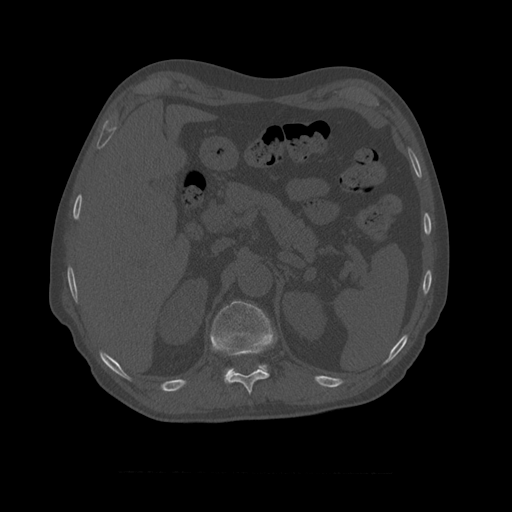
CT including the spine, one axial slice. Reconstruction kernel STANDARD. 120 kVp. Bone window (W 1800 / L 400 HU). 1.25 mm slice thickness. 512 × 512 image matrix, field of view 405 × 405 mm. Patient age 75 years. Case-level facts recorded for this patient, not image findings: primary cancer: prostate.
Structures marked on this image (semi-automatically segmented with operator editing):
- T10 vertebra: bounding box [x1, y1, x2, y2] px = [224, 345, 270, 395]
- T11 vertebra: [210, 301, 277, 382]